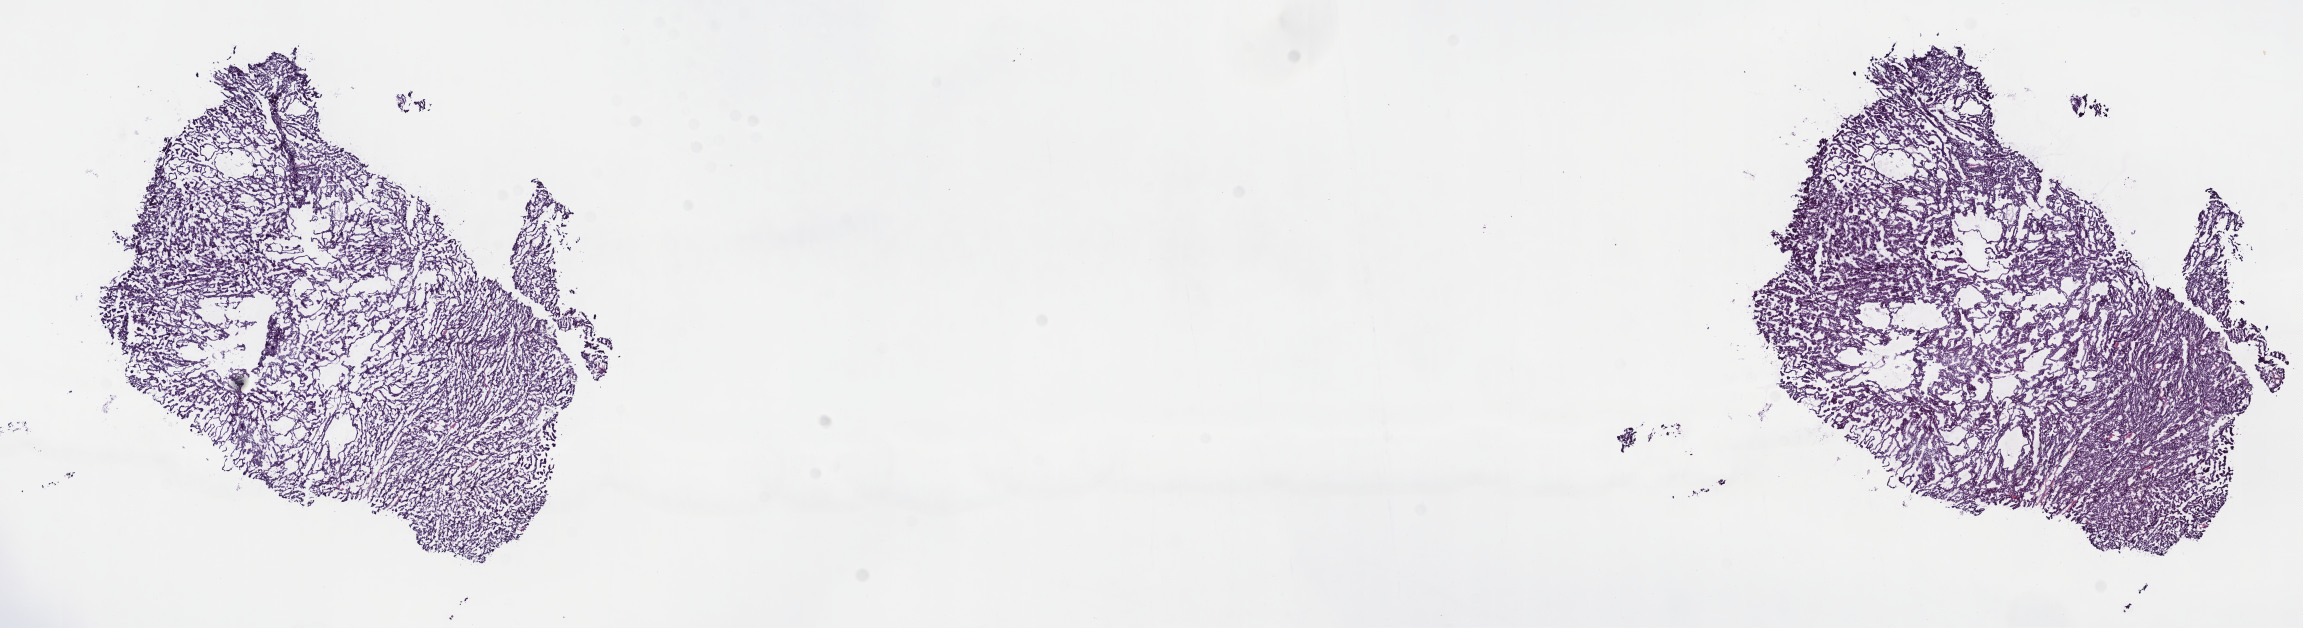
Digitized H&E tissue section (whole slide), a low-resolution overview of the entire scanned area, about 18.6 x 5.1 mm, frozen section, kidney, primary tumour sample. Male, age 59 years at initial diagnosis. Composition of this section per pathologist review: tumour cells 80%, tumour nuclei 80%, normal cells 0%, stromal cells 20%, necrosis 0%. Infiltration values recorded for this section: lymphocyte infiltration 0%, monocyte infiltration 5%, neutrophil infiltration 0%.
Histologic diagnosis: Papillary adenocarcinoma, NOS. AJCC pathologic stage: I.